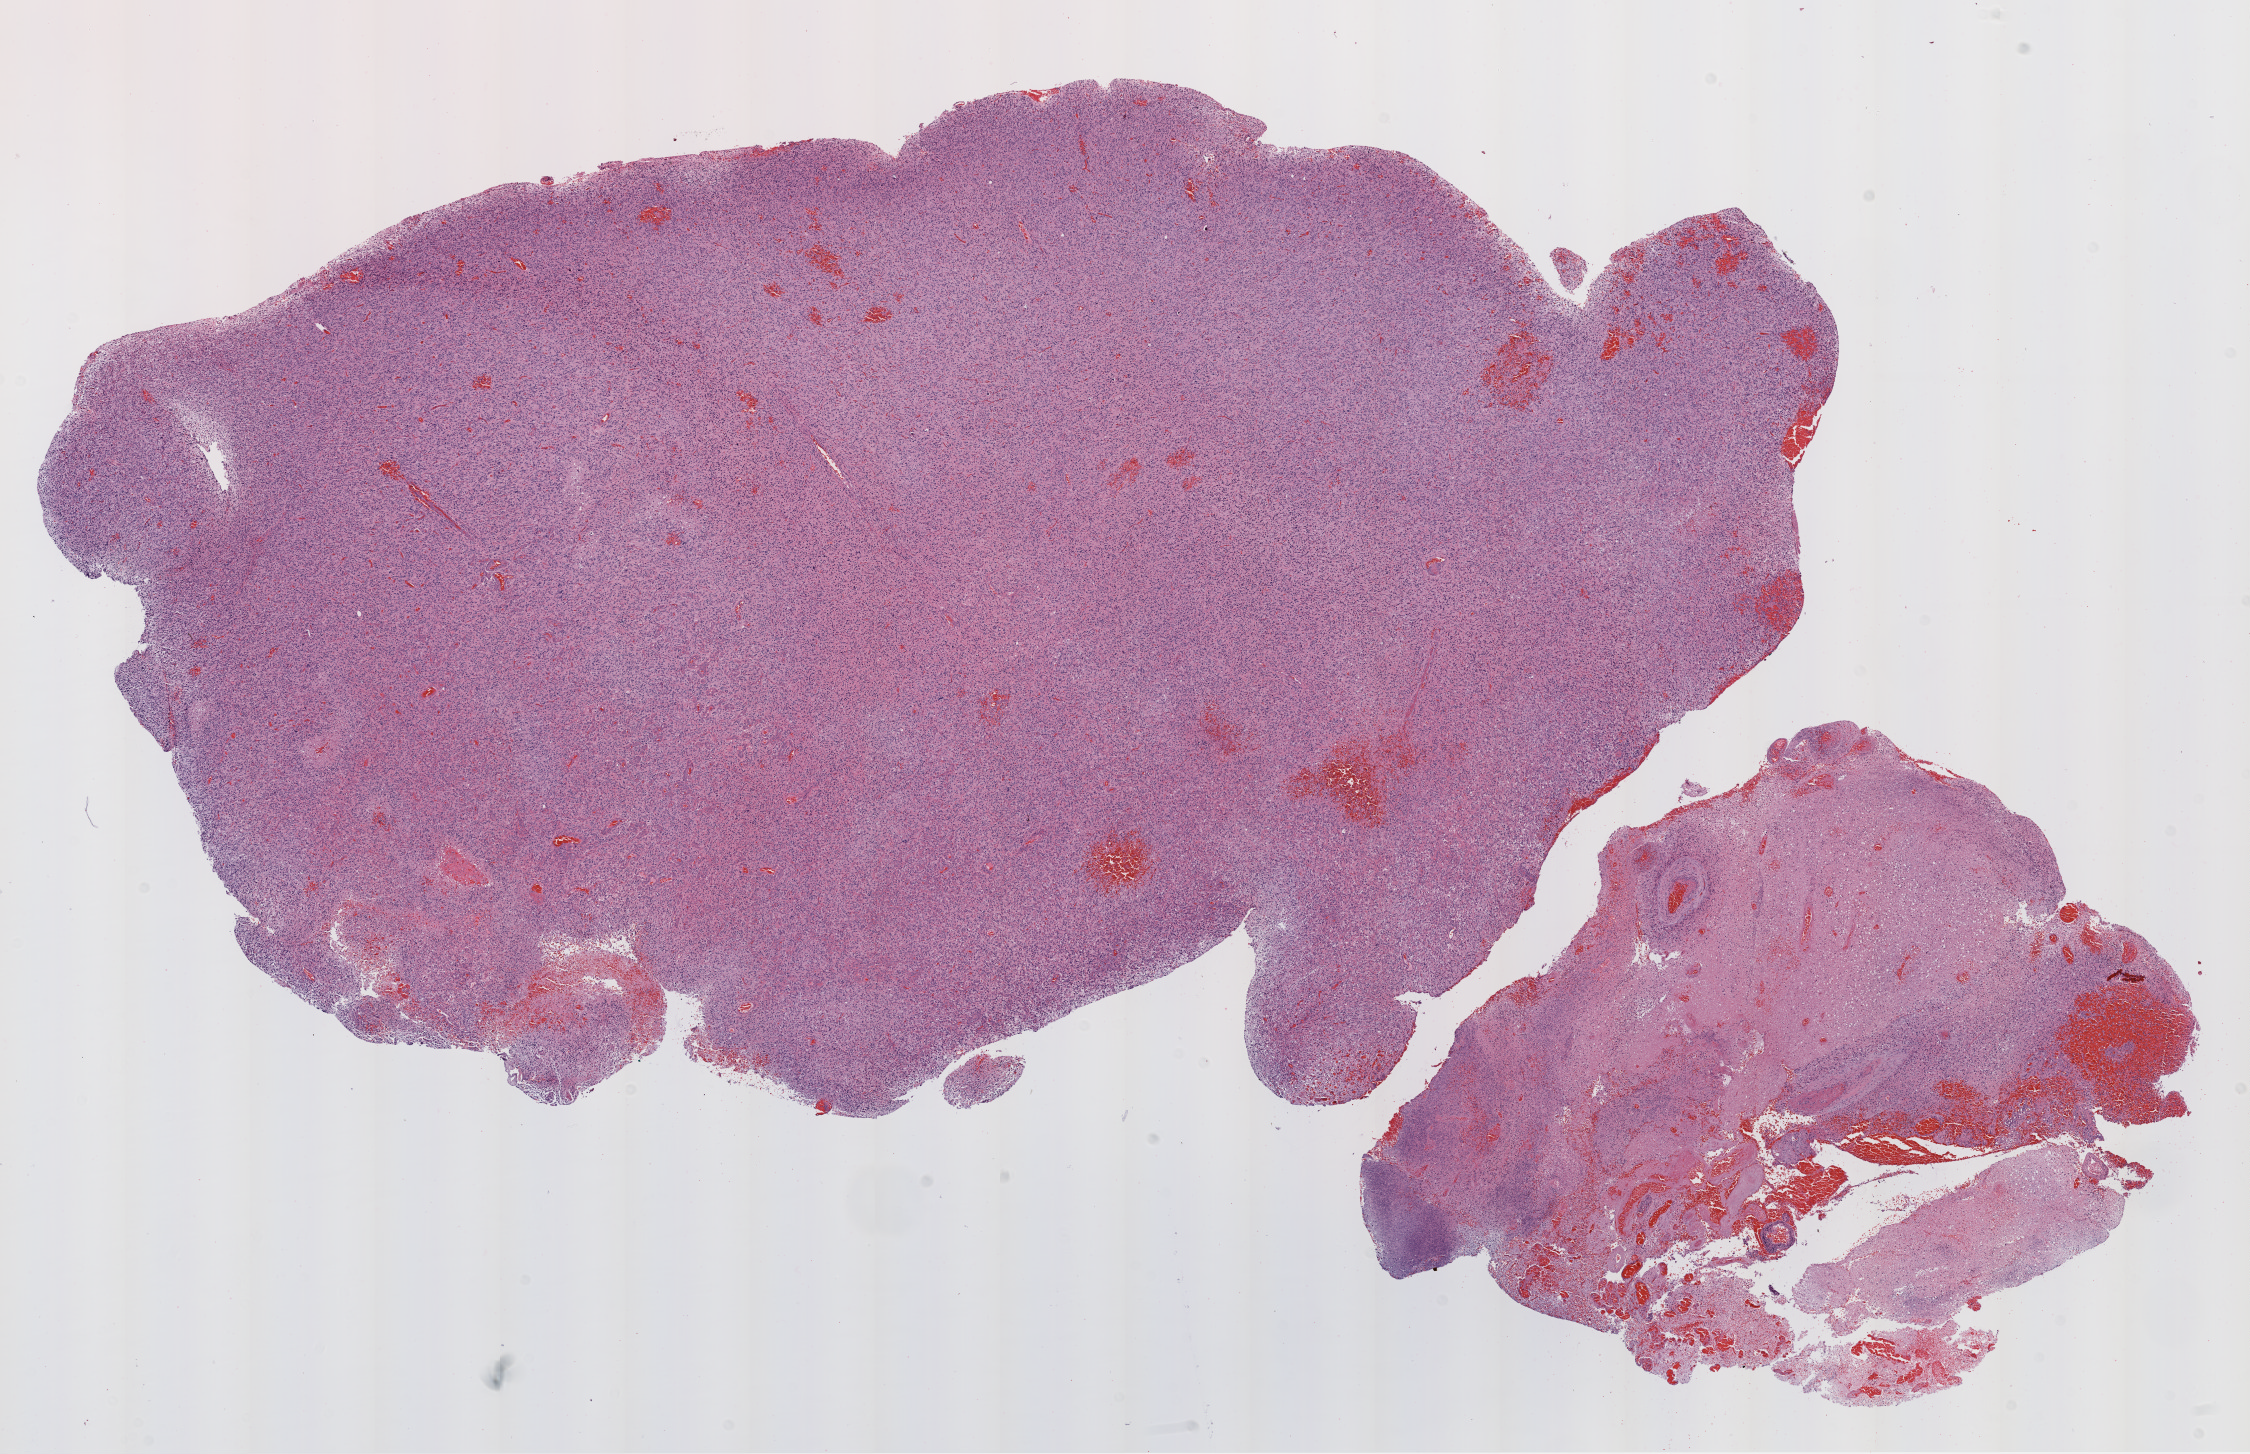
Whole-slide histology image, H&E-stained, shown as a low-resolution overview of the whole scanned area (about 18.1 x 11.7 mm, acquisition: 20x scan), FFPE section, brain, primary tumour sample. Male patient; age at initial diagnosis 43 years.
- diagnosis: Glioblastoma